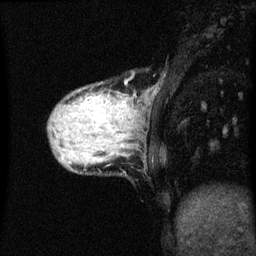
Breast MRI (dynamic contrast-enhanced), one sagittal slice; position 13 of 60 along the scan axis; dynamic contrast-enhanced series, image 2 of 3 at this slice position (ordered by acquisition); 1.5 T; TE 4.2 ms, TR 8.4 ms; 2 mm slice thickness; 256 × 256 image matrix, field of view 200 × 200 mm. Female patient, age 36 years.
Annotated regions visible in this slice (semi-automatic segmentation, software-assisted and operator-edited):
- analysis volume of interest (the breast-tissue region the enhancement analysis was run in; not a lesion): bounding box [x1, y1, x2, y2] px = [50, 82, 137, 151]
- tumour enhancement mask (voxels above the 70 % enhancement threshold inside the analysis volume of interest): [86, 96, 99, 101]